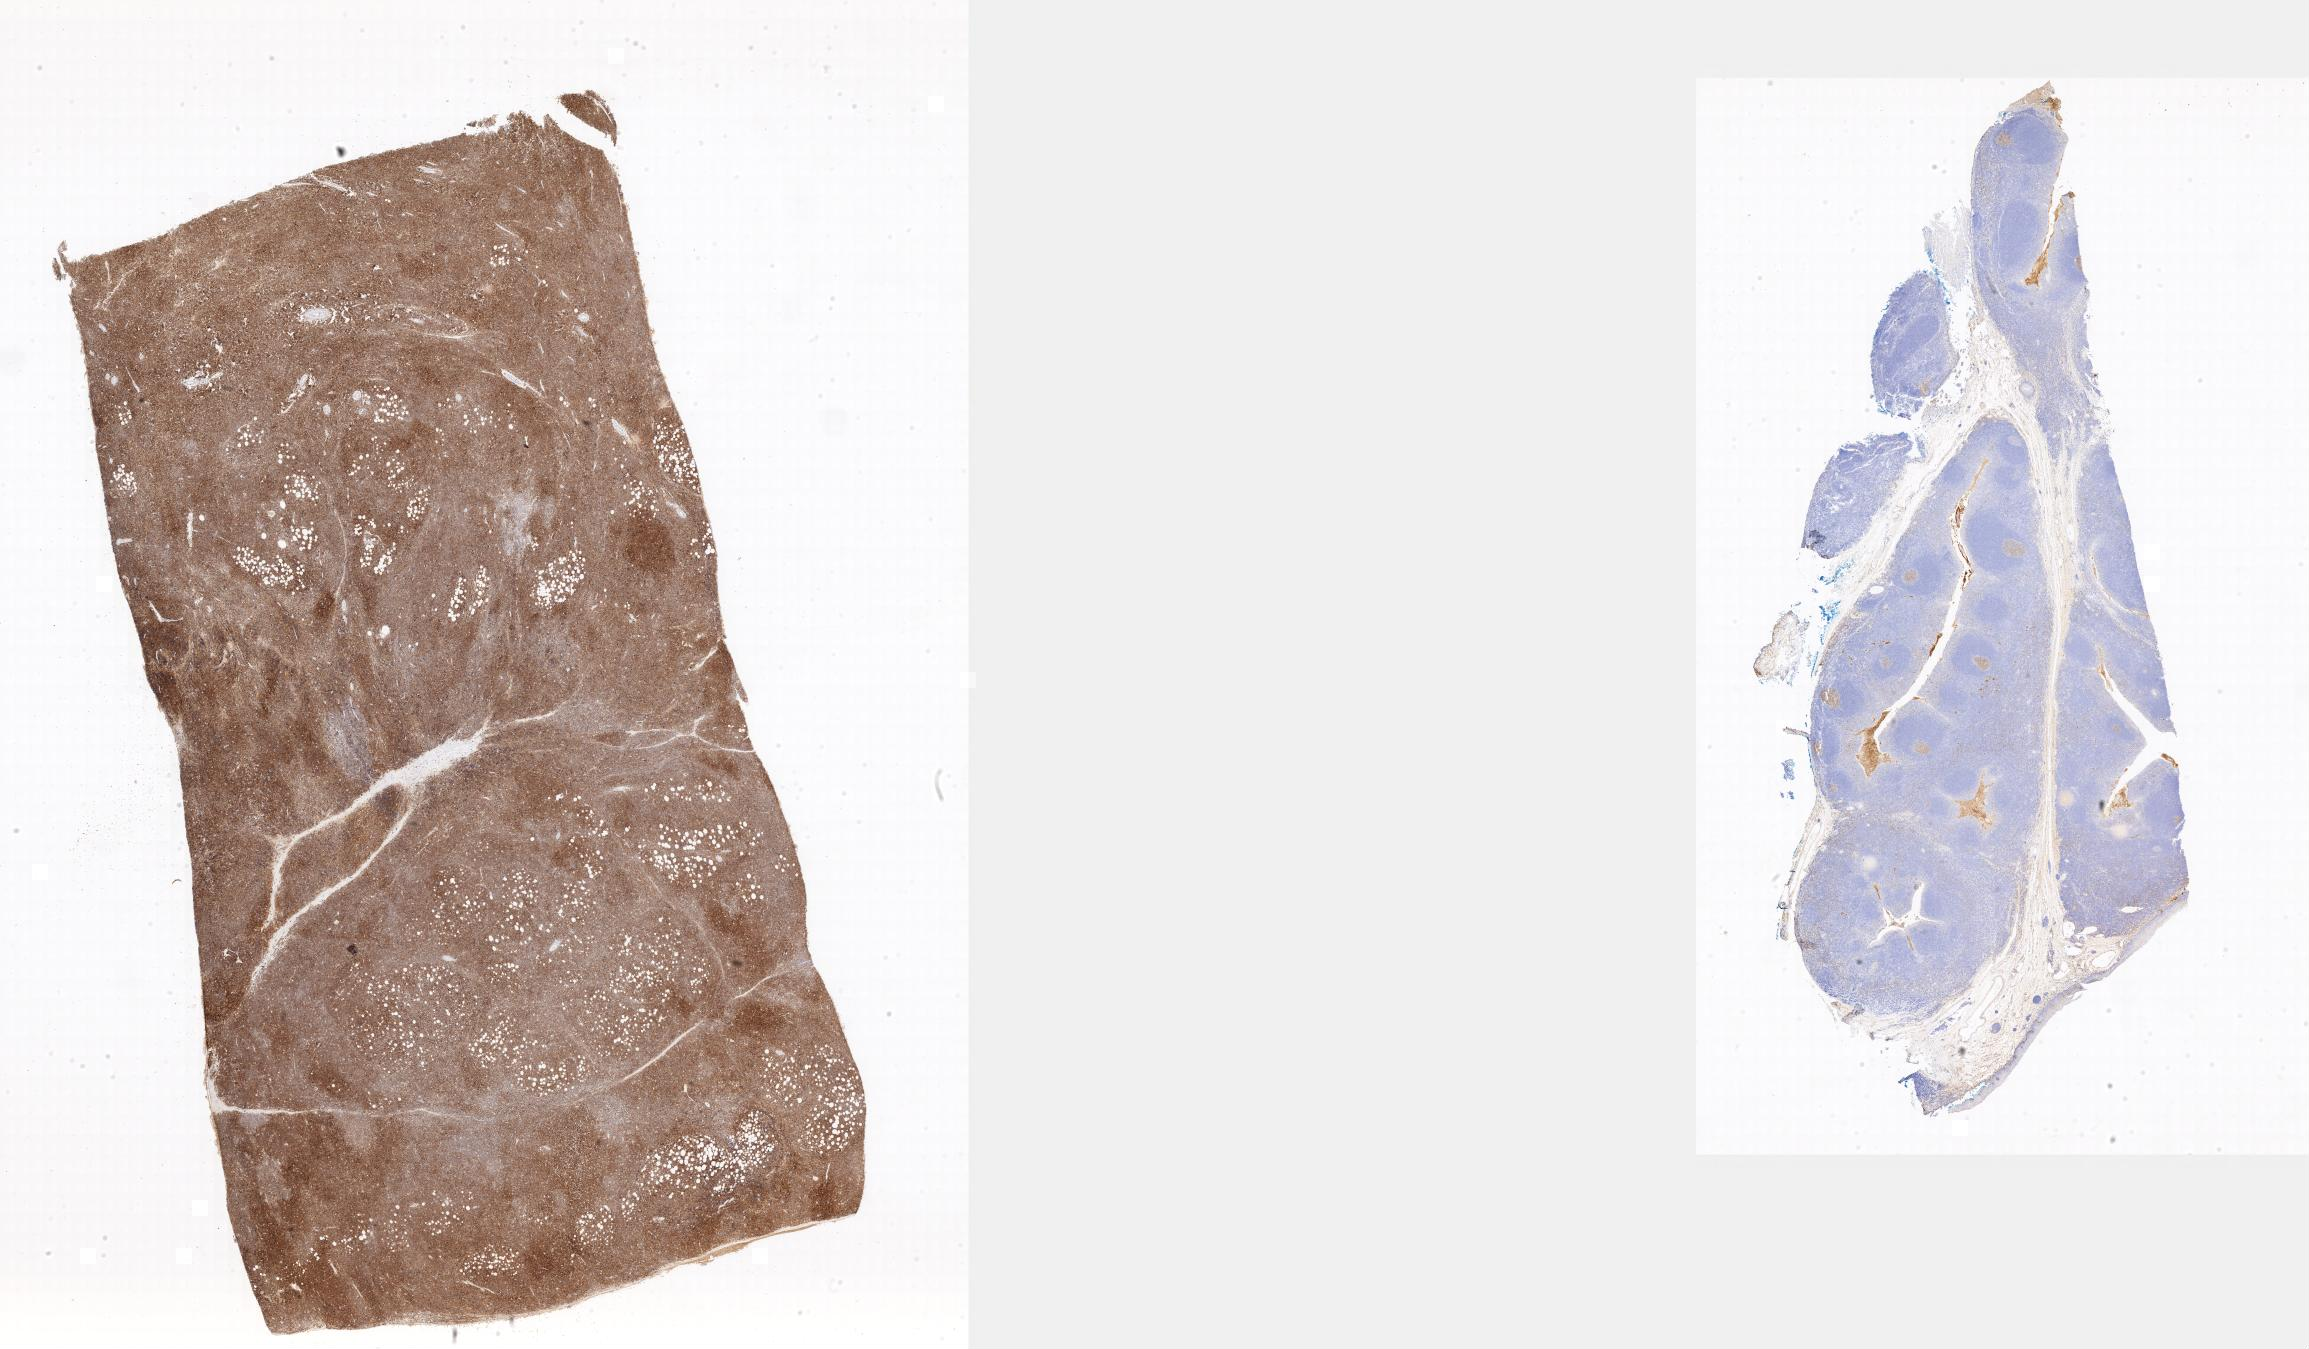
Immunohistochemistry (IHC) whole-slide image stained for CD10, a low-resolution overview of the entire scanned area. Specimen: tumor tissue. Site: colon. Female patient, 12 years old.
Histologic diagnosis: Burkitt lymphoma, NOS.